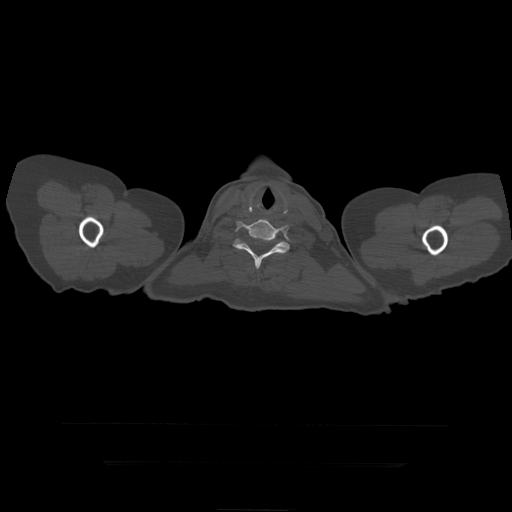
CT including the spine, one axial slice; slice 396 of 399 in the series (ordered by position); 120 kVp; bone window (W 1800 / L 400 HU); 1.25 mm slice thickness; 512 × 512 image matrix. Patient age 41 years. Case-level facts recorded for this patient, not image findings: primary cancer: breast.
Outlined on this slice (semi-automatic segmentation, software-assisted and operator-edited):
- T1 vertebra: bounding box [x1, y1, x2, y2] px = [233, 238, 290, 254]